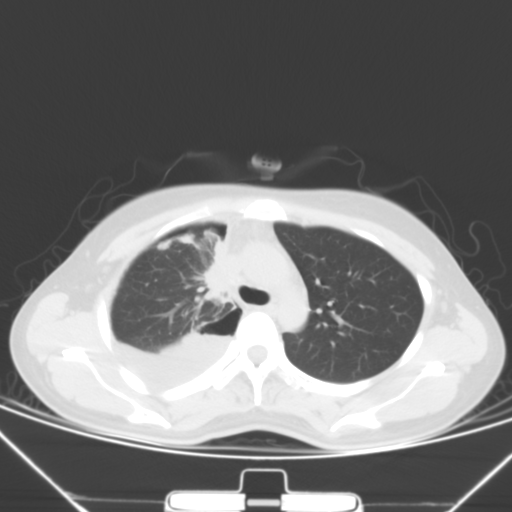
Chest CT, one axial slice; slice 40 of 57 in the series (ordered by position); lung window (W 1500 / L -600 HU); 512 × 512 image matrix, field of view 343 × 343 mm. Female patient, age 28 years. Case-level facts recorded for this patient, not image findings: clinical TNM (as recorded): T2 N0 M1a.
Annotated regions visible in this slice (rectangle marked by the reading radiologist):
- lung tumour (recorded histology: adenocarcinoma): bounding box (x1, y1, x2, y2) in pixels: (198, 243, 244, 309)